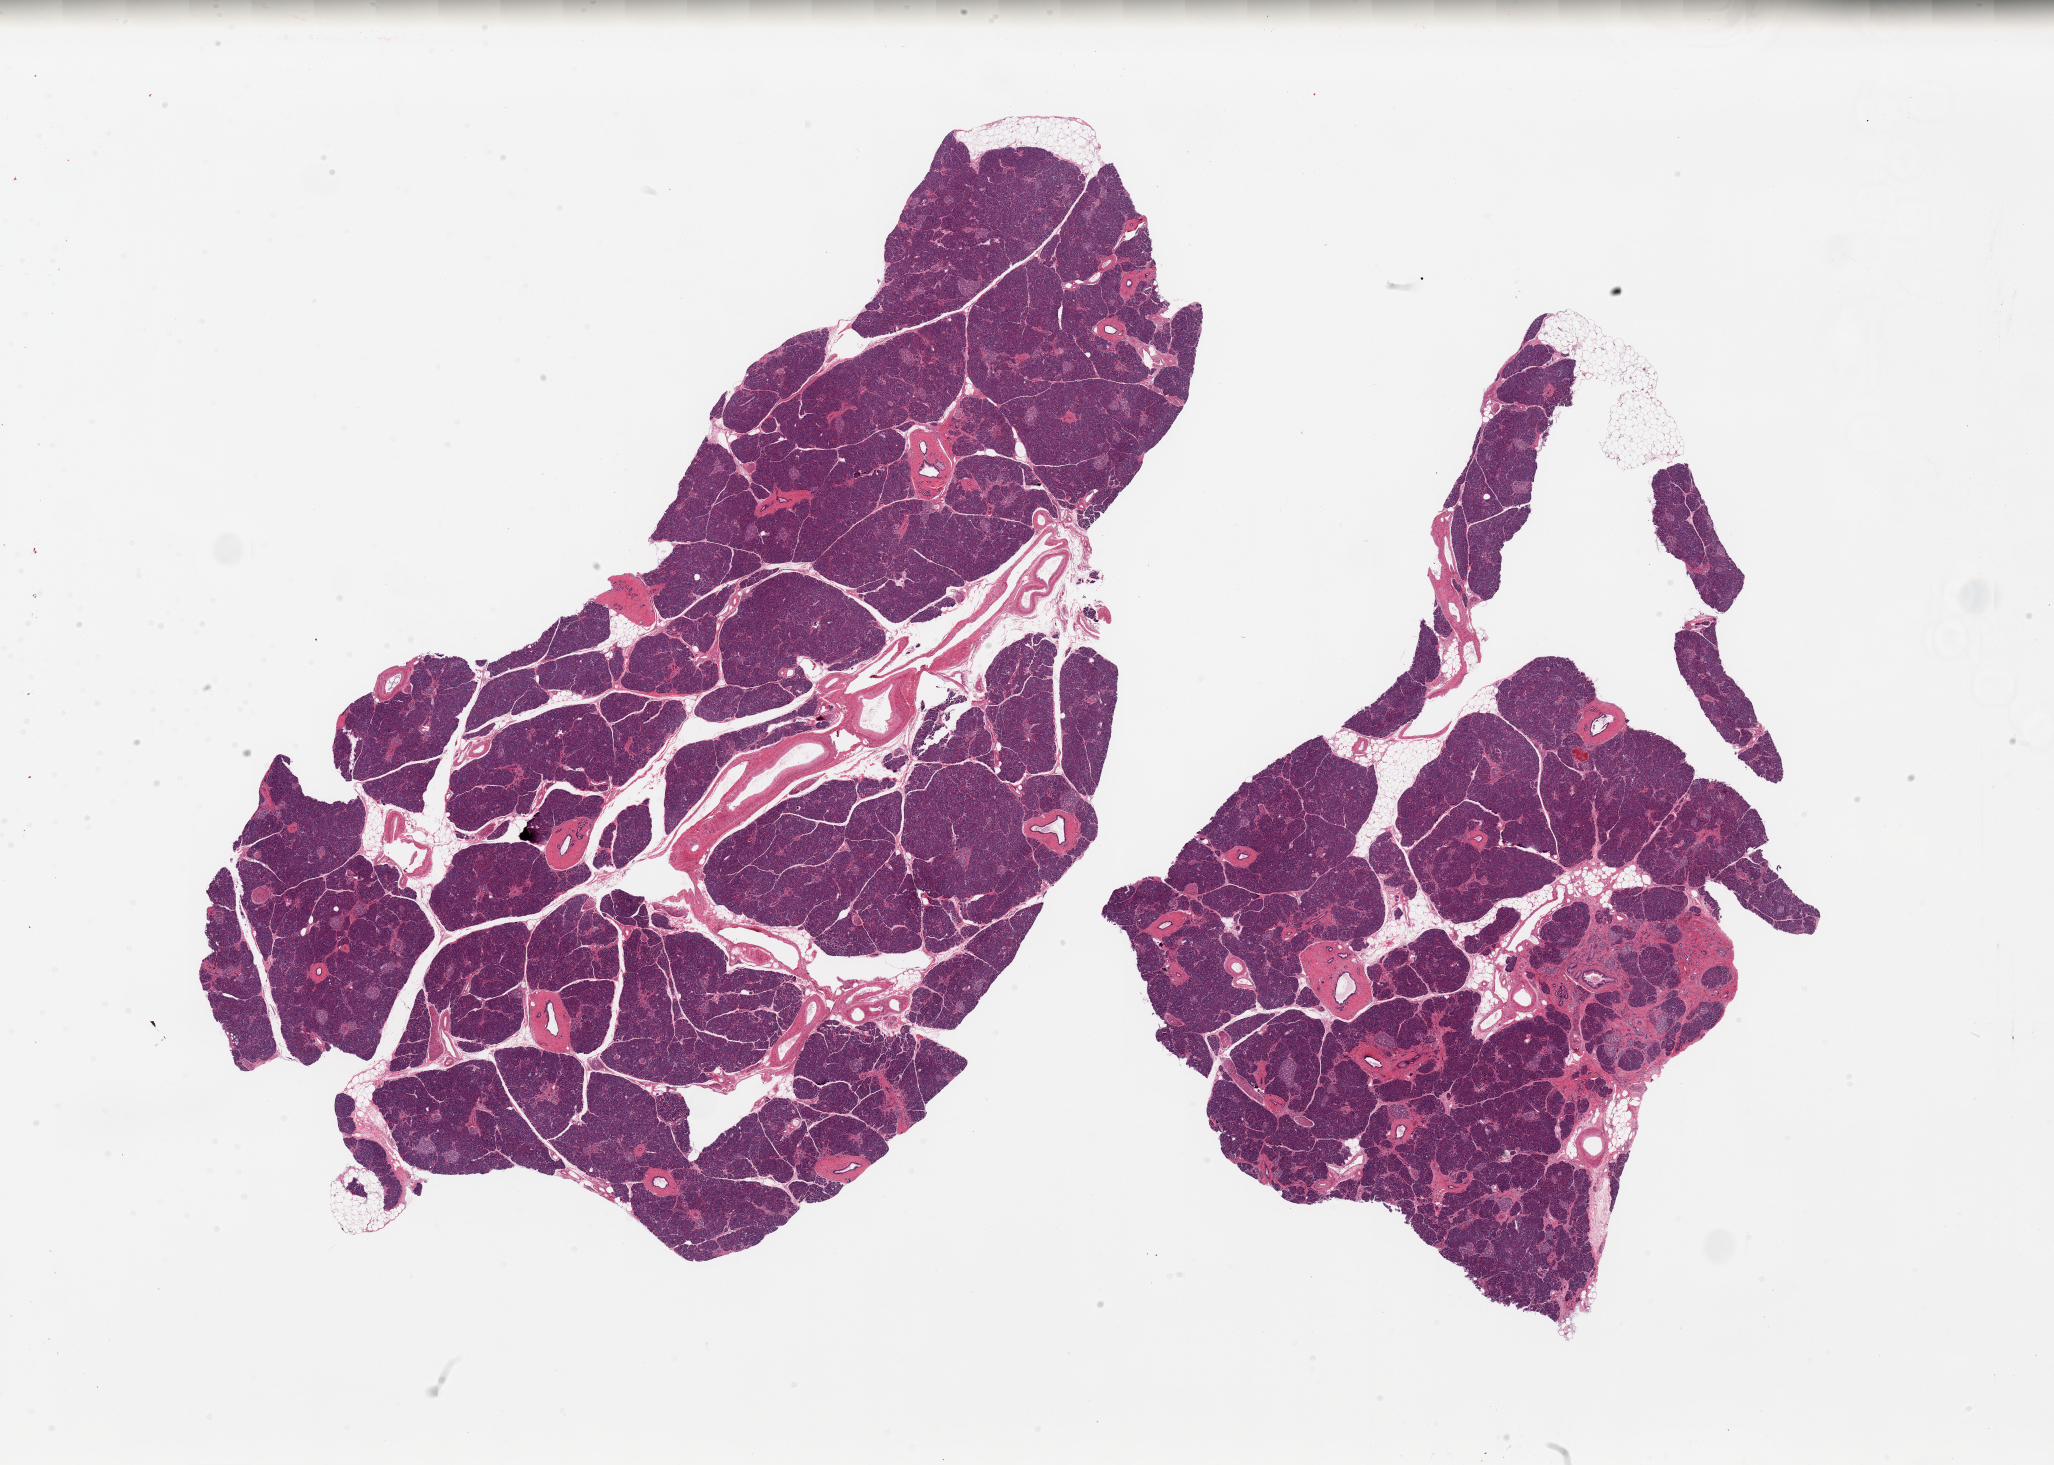
Digitized H&E-stained section — whole scanned area (about 32.5 x 23.2 mm, acquisition: 20x scan) shown as a low-resolution overview. PAXgene-fixed paraffin-embedded (PFPE) section. Sampled site (target tissue): pancreas. Tissue donor sample. Male donor.
Reviewer comment on this tissue sample: 2 pieces; well preserved parenchyma with prominent islets, periductal fibrosis and focal interstitial fibrosis with relative increase of islets, ~10% internal fat.